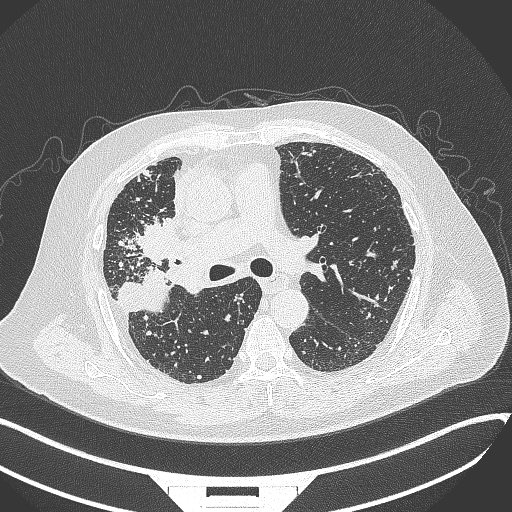
Chest CT, one axial slice. Slice 211 of 384 in the series (ordered by position). Reconstruction kernel B70f. 120 kVp. Lung window (W 1500 / L -600 HU). 1 mm slice thickness. 512 × 512 image matrix. Male patient, age 69 years. Case-level facts recorded for this patient, not image findings: clinical TNM (as recorded): T4 N3 M1.
Structures marked on this image (bounding box drawn by a radiologist):
- lung tumour (recorded histology: adenocarcinoma): bounding box (x1, y1, x2, y2) in pixels: (136, 212, 191, 275)